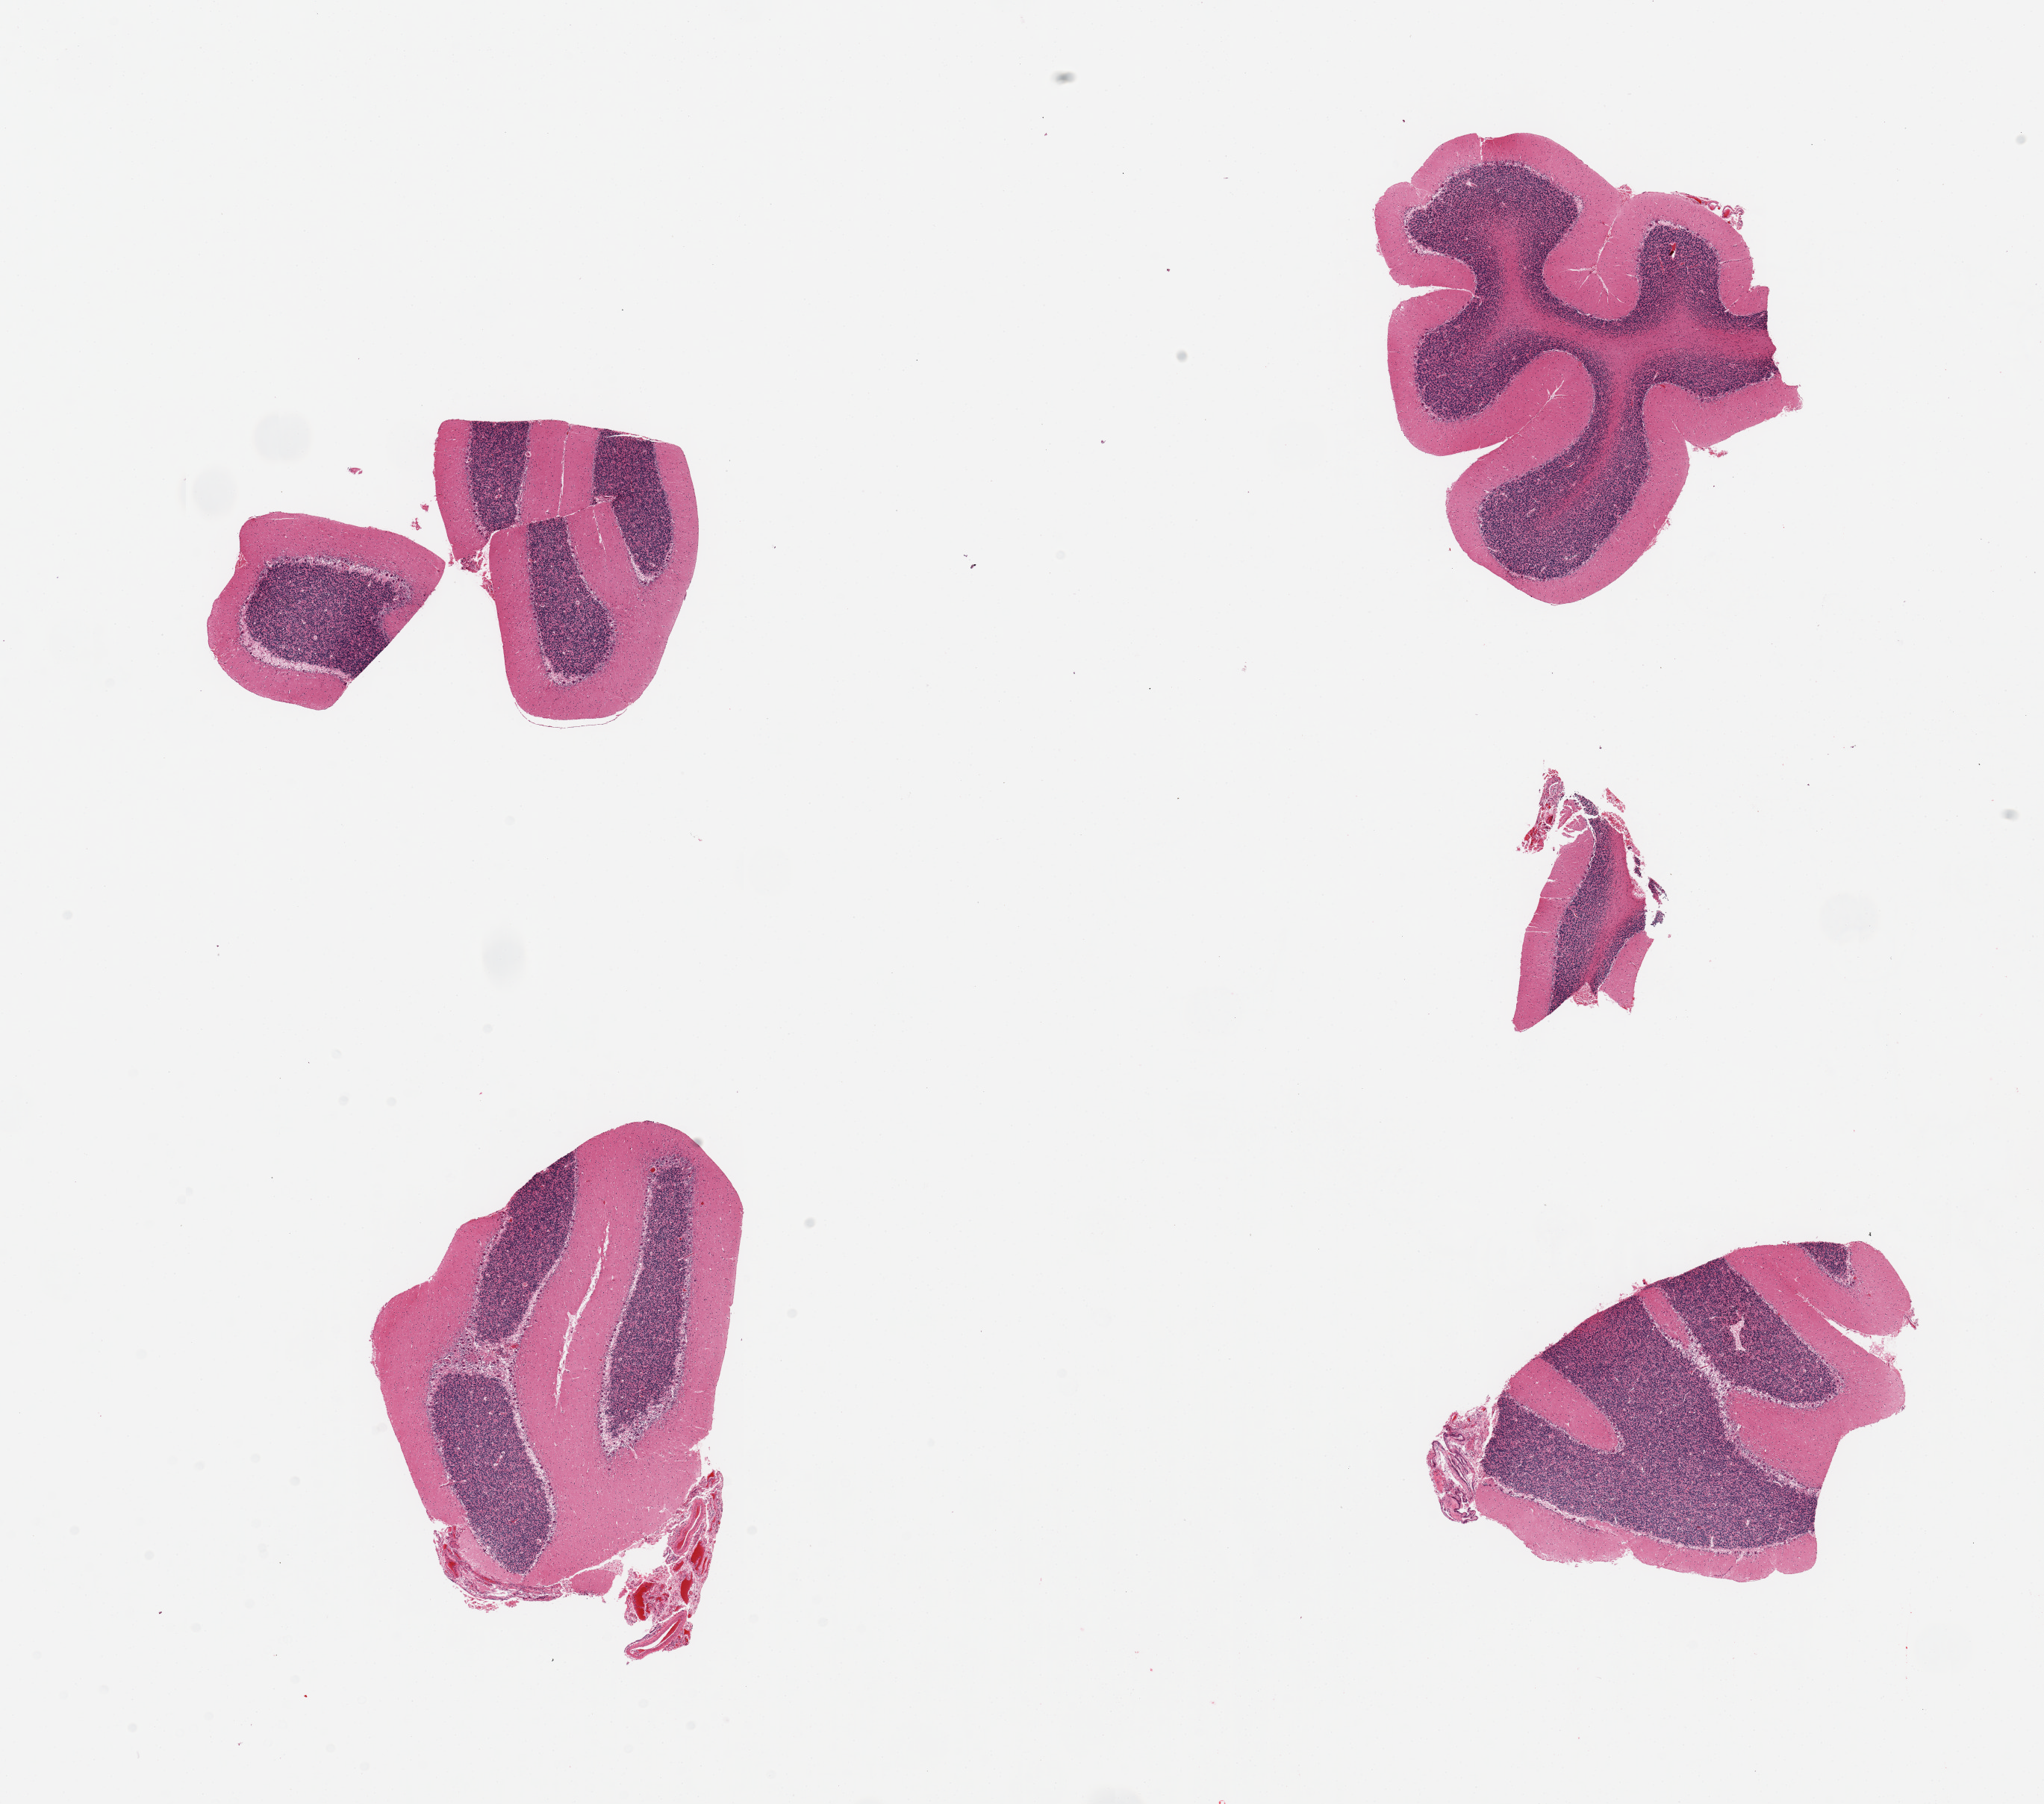
Whole-slide image, H&E stain, a low-resolution overview of the entire scanned area, about 21.7 x 19.1 mm; PAXgene-fixed, paraffin-embedded tissue; target tissue: cerebellum; tissue donor sample.
Review note (as recorded): 4 pieces.